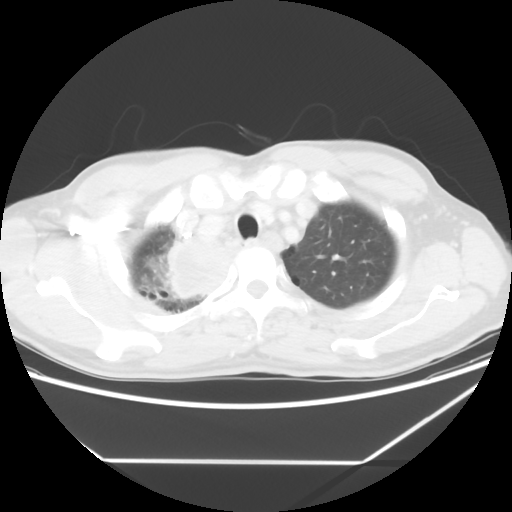
Chest CT, one axial slice; position 52 of 60 along the scan axis; reconstruction kernel STANDARD; 120 kVp; lung window (W 1500 / L -600 HU); 5 mm slice thickness; 512 × 512 image matrix, field of view 367 × 367 mm. Patient: male, 58 years. From the clinical record (not read from this slice): clinical TNM (as recorded): T2 N2 M0.
Structures marked on this image (bounding box drawn by a radiologist):
- lung tumour (recorded histology: squamous cell carcinoma): bounding box <160,230,234,303> (left, top, right, bottom; pixels)